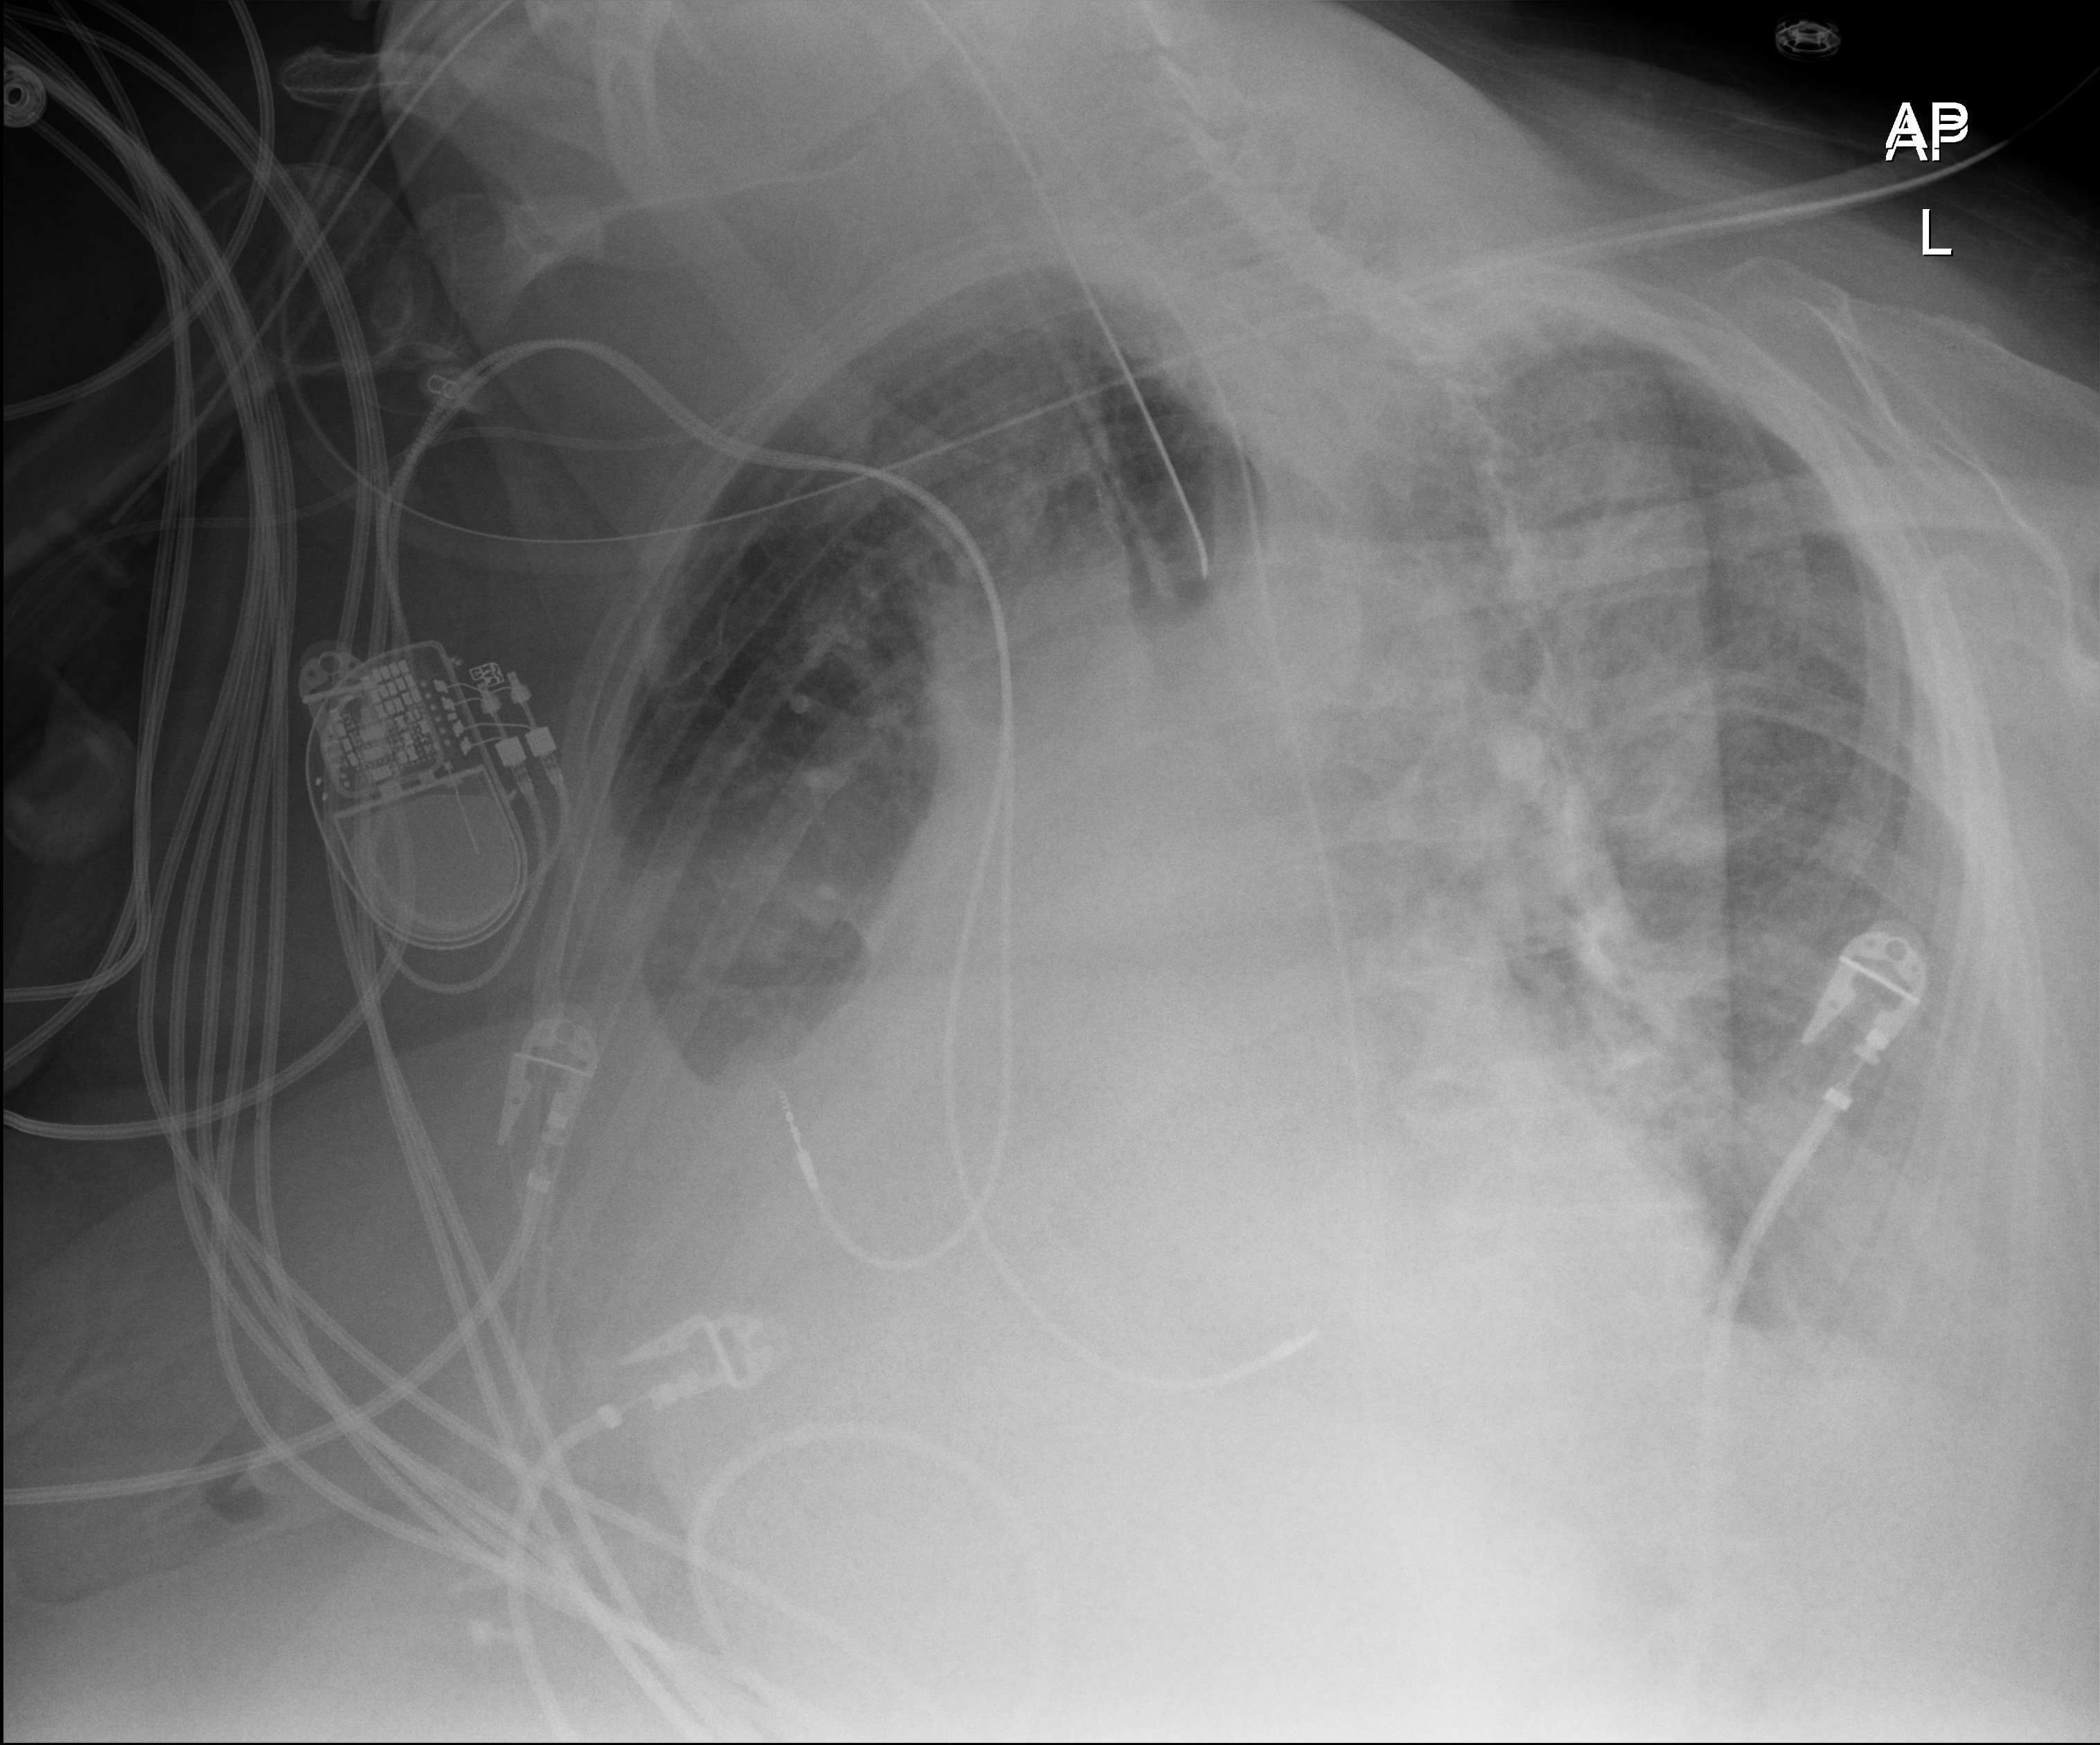
Portable chest radiograph, anteroposterior (AP) projection. Female patient hospitalised with COVID-19, age 75–90 years.
Hospital-stay facts (about this admission, not read from this image; timing relative to this image not recorded): admitted to intensive care during this hospital stay: yes; mechanically ventilated during this hospital stay: yes; hypertension (admission record): yes.